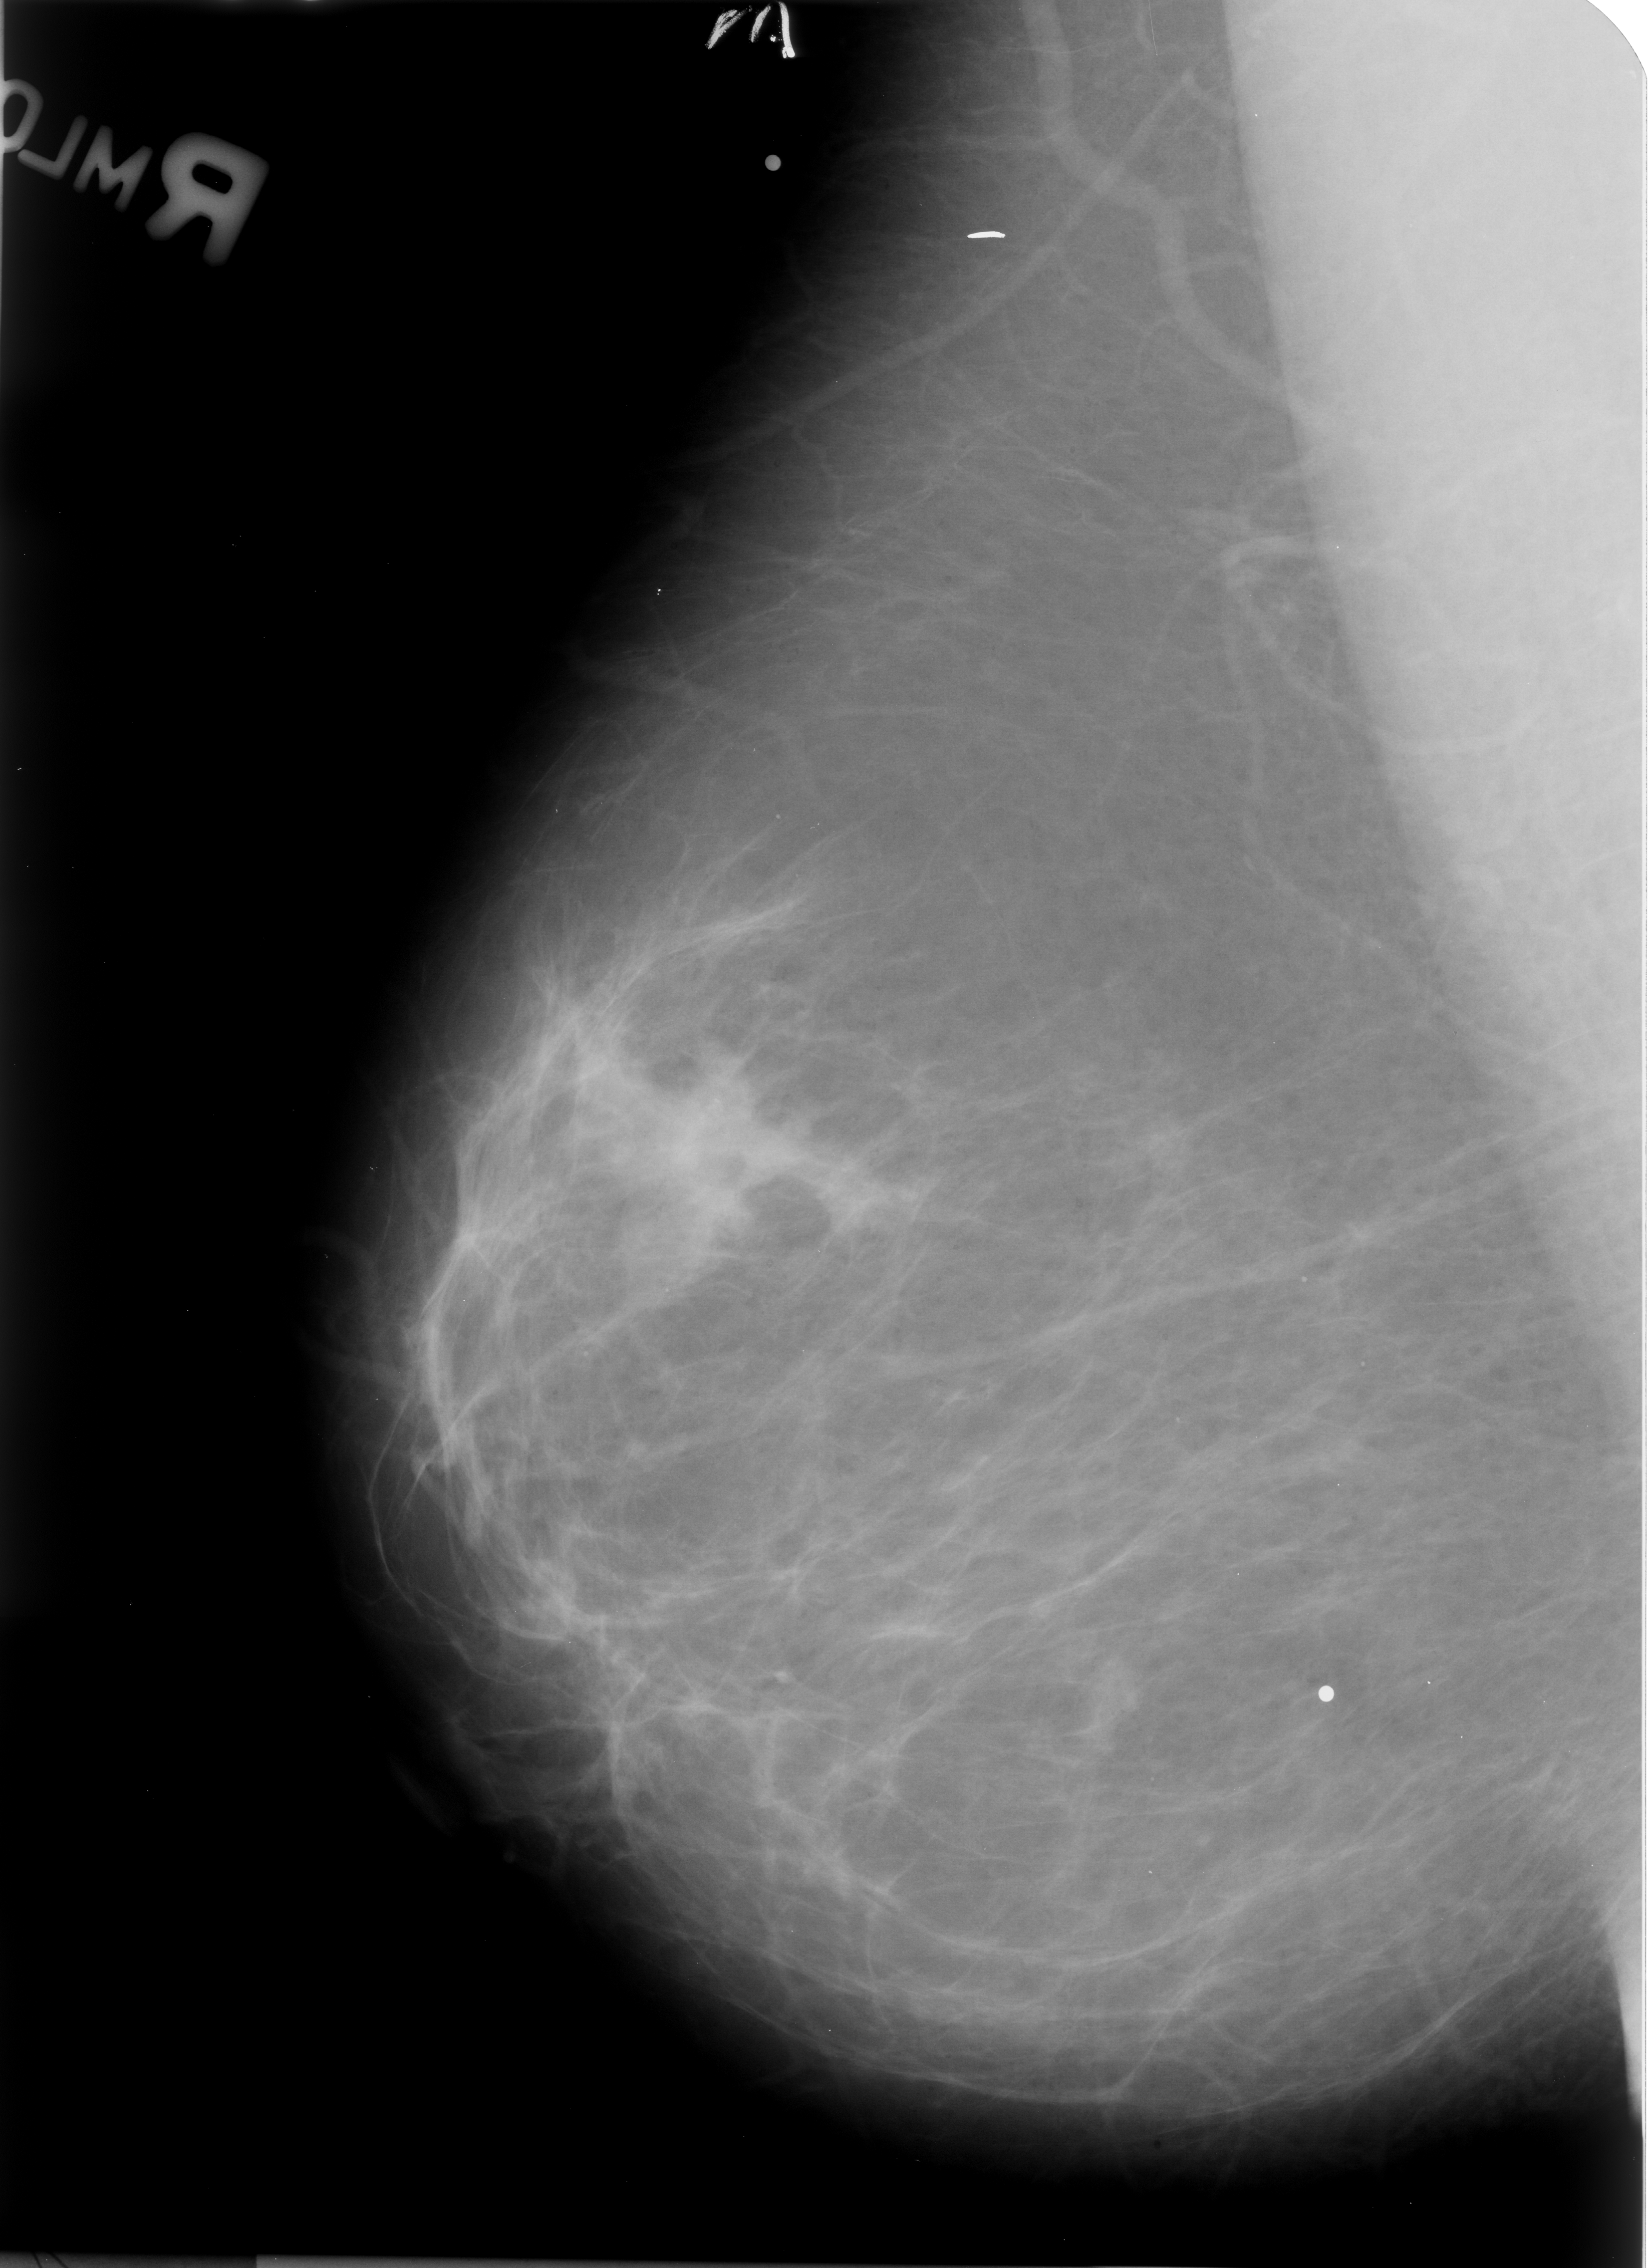
Digitized screen-film mammogram, right breast, MLO view, breast composition: almost entirely fatty (BI-RADS density category 1 of 4).
Marked findings (only marked abnormalities are described; nothing is implied about the rest of the image): mass, shape irregular / architectural distortion, margins ill defined / spiculated; BI-RADS assessment category 4; pathology result (as recorded, not read from the image): malignant.